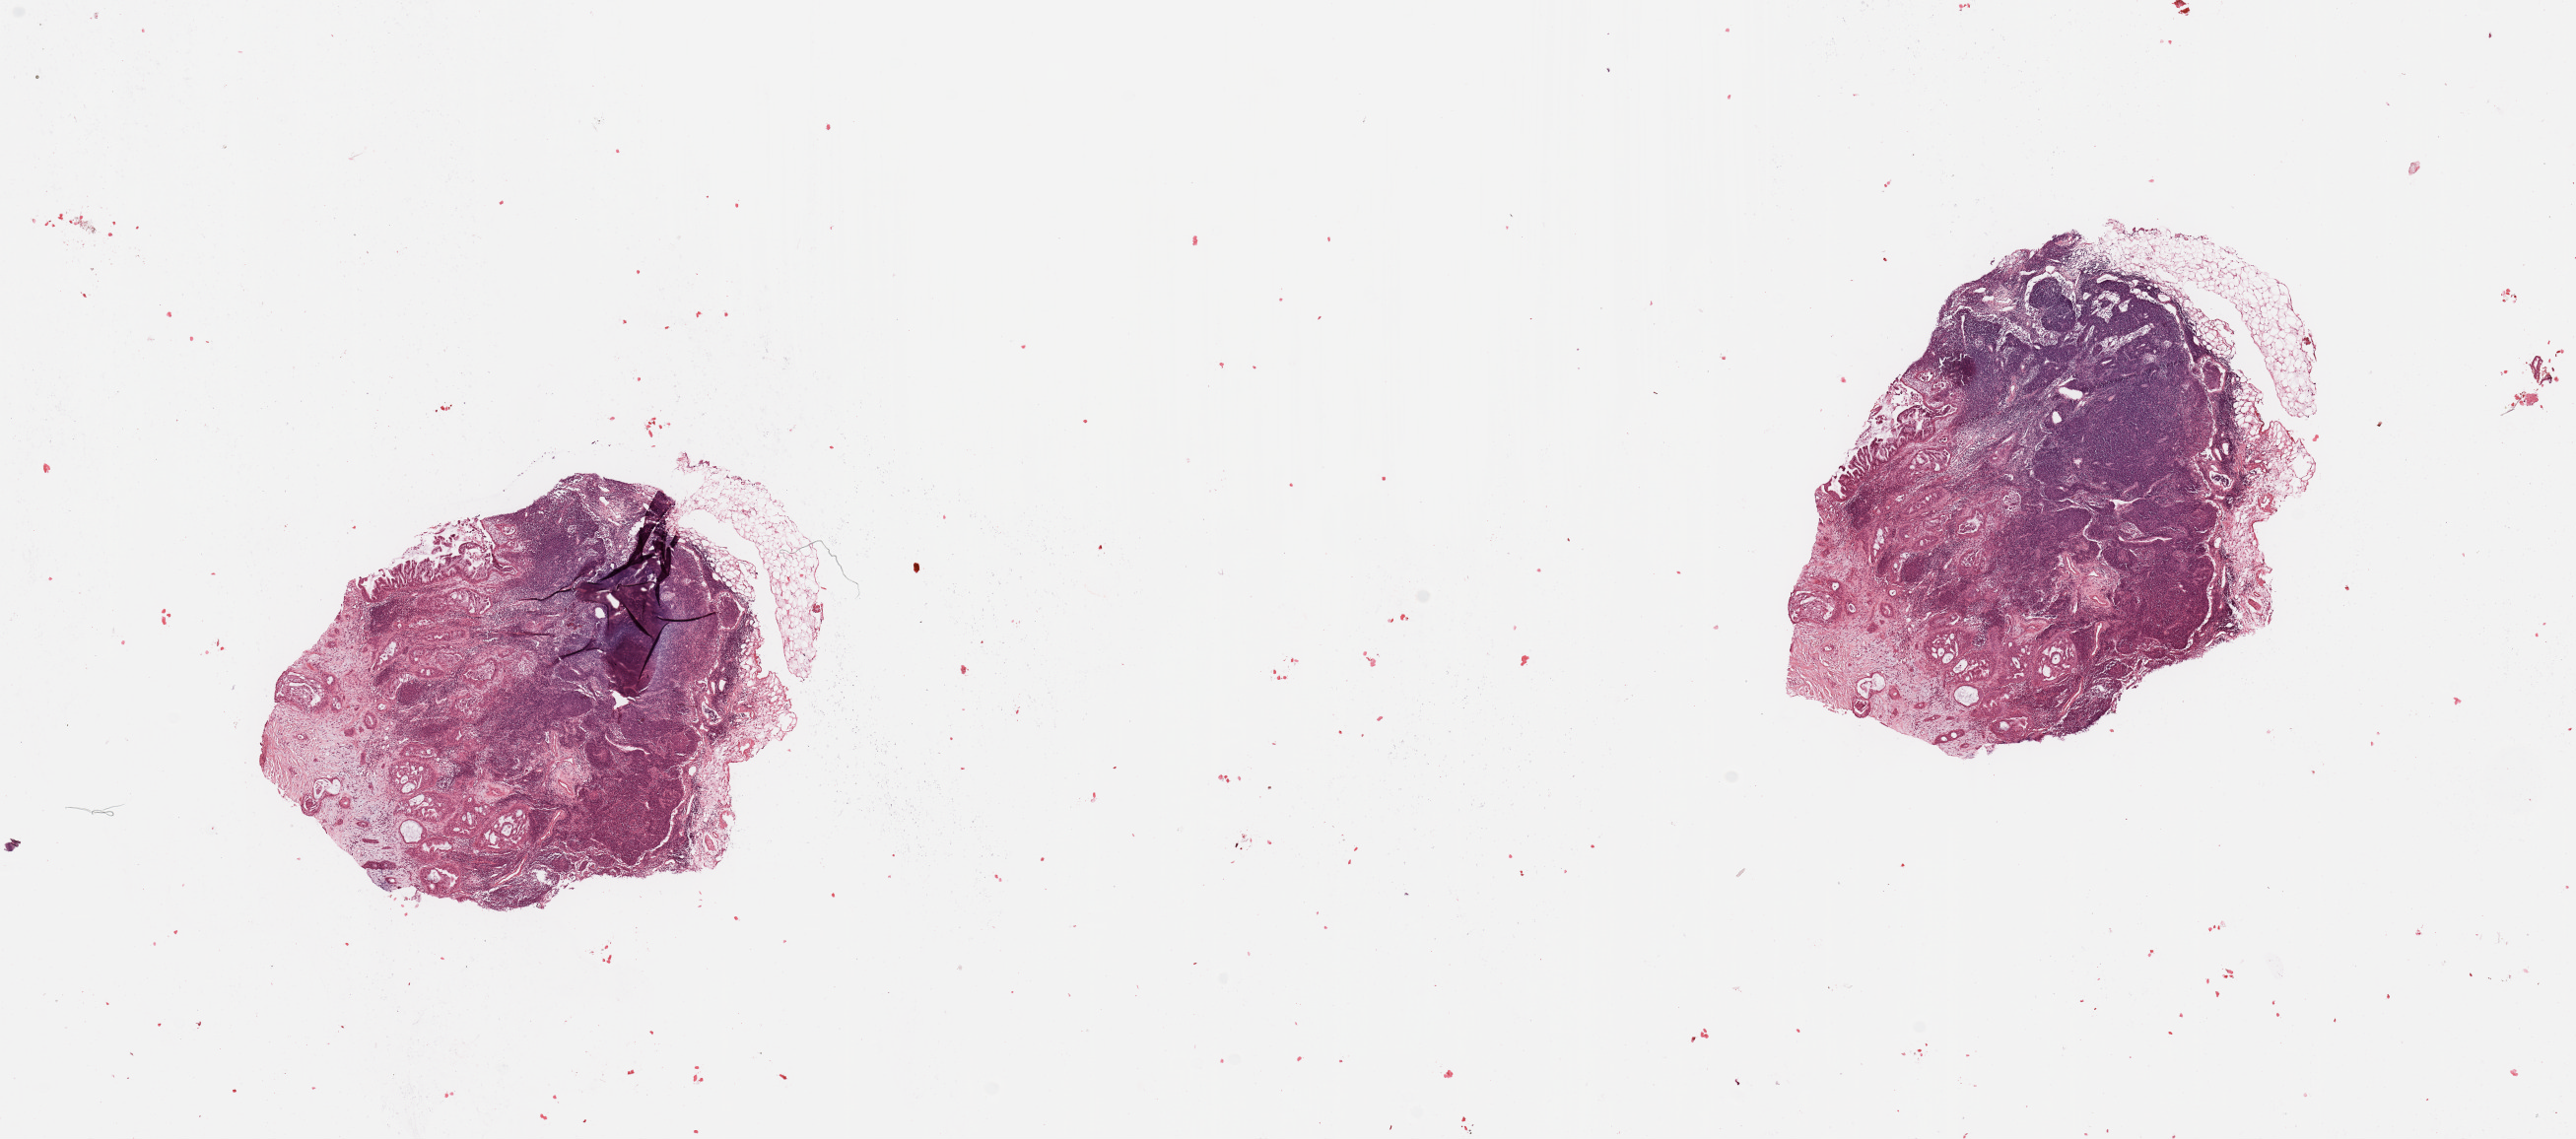
Whole-slide histology image, H&E-stained — whole scanned area (about 20.7 x 9.1 mm, slide scanned at 20x) shown as a low-resolution overview. Normal (non-tumour) tissue sample, pancreas. Male, 68 y/o.
This section: normal (non-tumour) tissue from the same patient. Patient diagnosis: Infiltrating duct carcinoma, NOS.